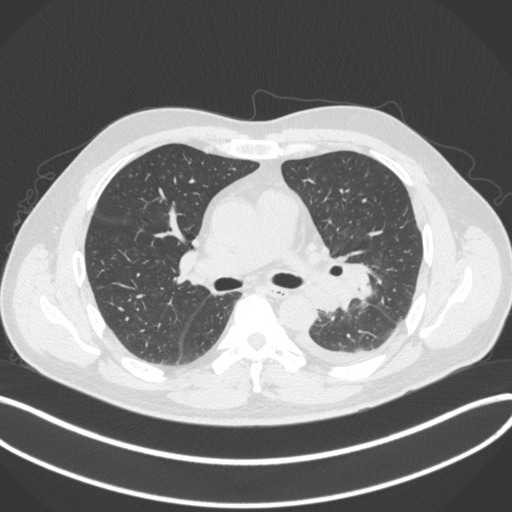
Chest CT, one axial slice; reconstruction kernel B31f; 120 kVp; lung window (W 1500 / L -600 HU); 512 × 512 image matrix, field of view 400 × 400 mm. Male patient, age 58 years. Case-level facts recorded for this patient, not image findings: clinical TNM (as recorded): T3 N1 M1b; histopathological grade: G3.
Annotated regions visible in this slice (bounding box drawn by a radiologist):
- lung tumour (recorded histology: small cell carcinoma): bounding box [x1, y1, x2, y2] px = [336, 259, 376, 312]